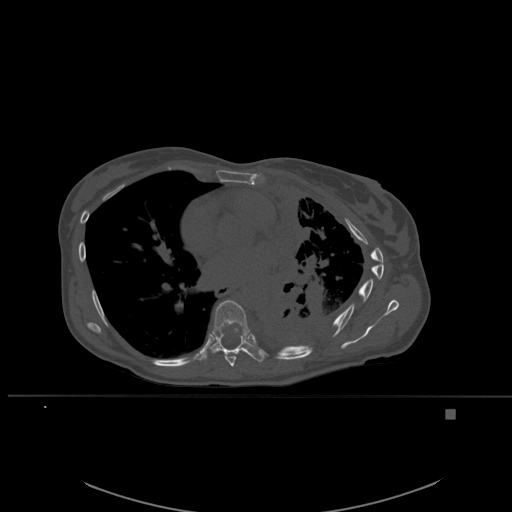
CT including the spine, one axial slice; slice 356 of 537 in the series (ordered by position); bone window (W 1800 / L 400 HU); 512 × 512 image matrix, field of view 440 × 440 mm. Female patient, age 45 years. Case-level facts recorded for this patient, not image findings: primary cancer: lung.
Annotated regions visible in this slice (semi-automatic segmentation, software-assisted and operator-edited):
- T7 vertebra: box from (x=220, y=350) to (x=243, y=367) px
- T8 vertebra: (x=196, y=300)–(x=264, y=363)